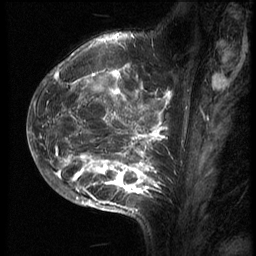
Breast MRI (dynamic contrast-enhanced), one sagittal slice. Slice 24 of 70 in the series (ordered by position). 3 images stored at this slice position (order not interpretable as contrast timing). 1.5 T. TE 4.2 ms, TR 9 ms. 2.5 mm slice thickness. 256 × 256 image matrix, field of view 180 × 180 mm. Female patient, age 28 years. From the clinical record (not read from this slice): setting: breast cancer imaged before/during neoadjuvant chemotherapy.
Structures marked on this image (semi-automatic segmentation, software-assisted and operator-edited):
- analysis volume of interest (the breast-tissue region the enhancement analysis was run in; not a lesion): bounding box (x1, y1, x2, y2) in pixels: (43, 42, 186, 215)
- tumour enhancement mask (voxels above the 140 % enhancement threshold inside the analysis volume of interest): (45, 55, 172, 210)